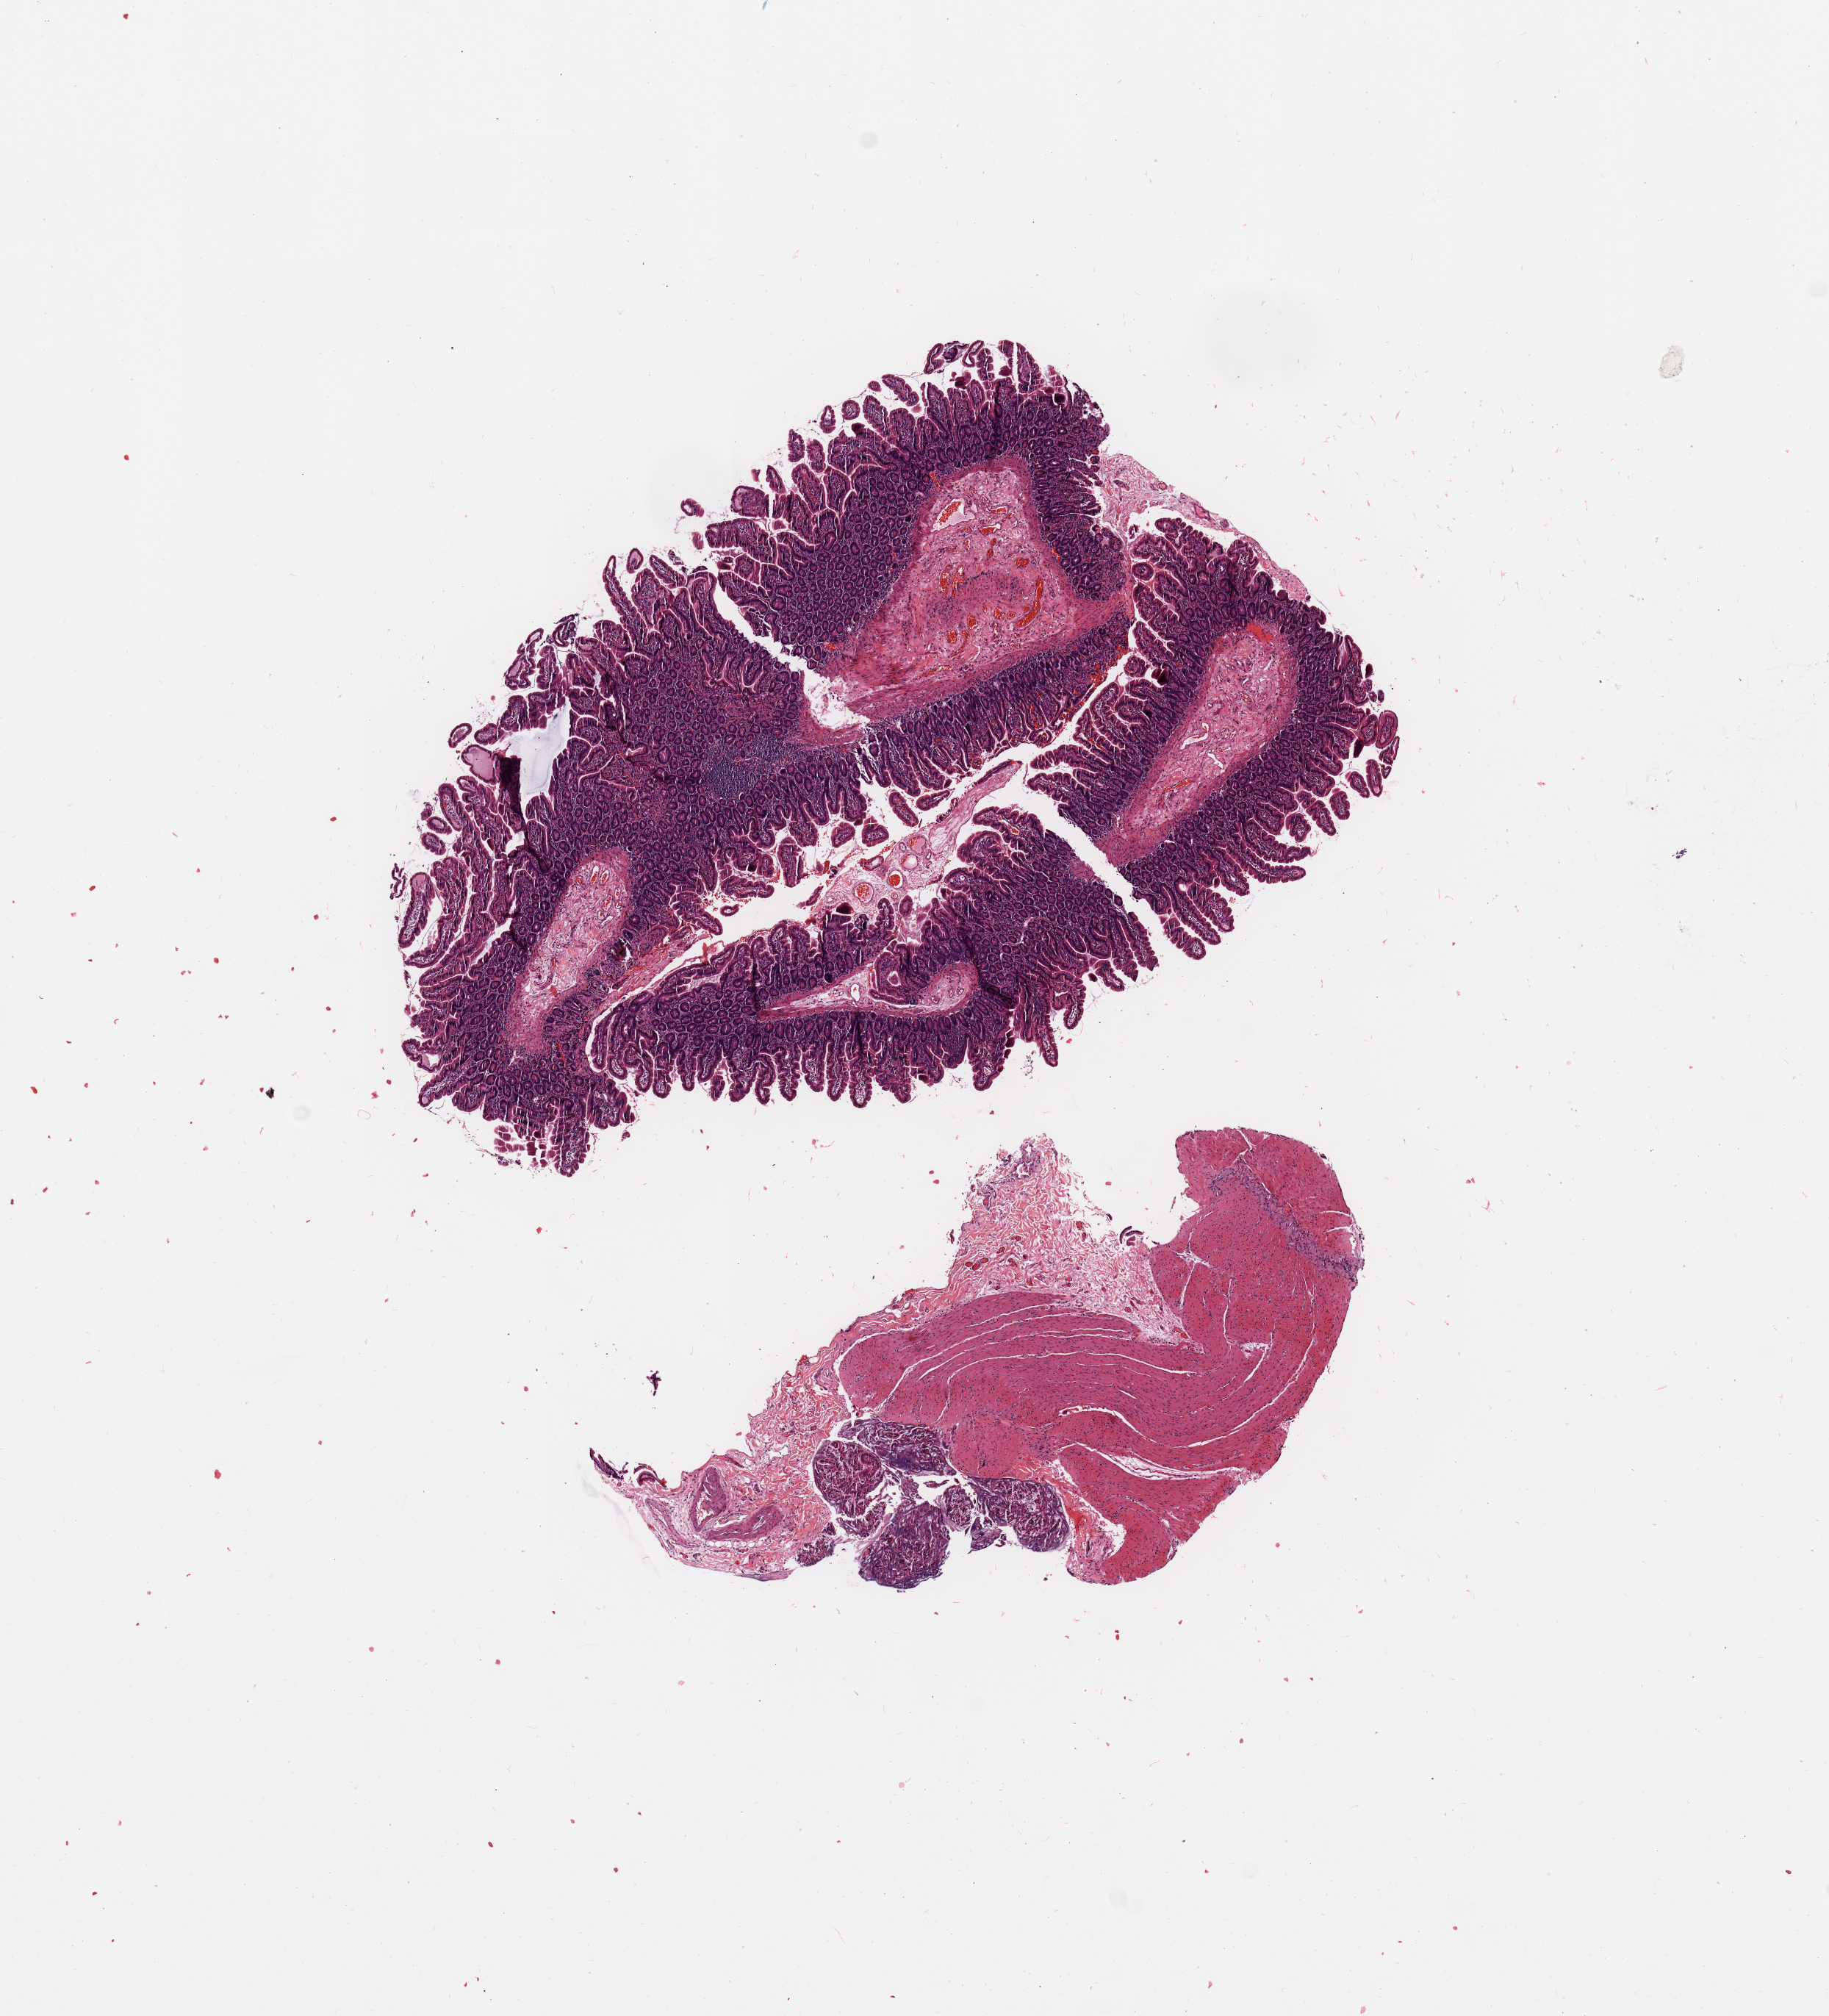
Digitized Hematoxylin and eosin (H&E) stained tissue section (whole slide), a low-resolution overview of the entire scanned area, about 9.8 x 10.8 mm. Pancreas, normal (non-tumour) tissue. Patient: male, age 63 years.
This section: normal (non-tumour) tissue from the same patient. Patient diagnosis: Infiltrating duct carcinoma, NOS.